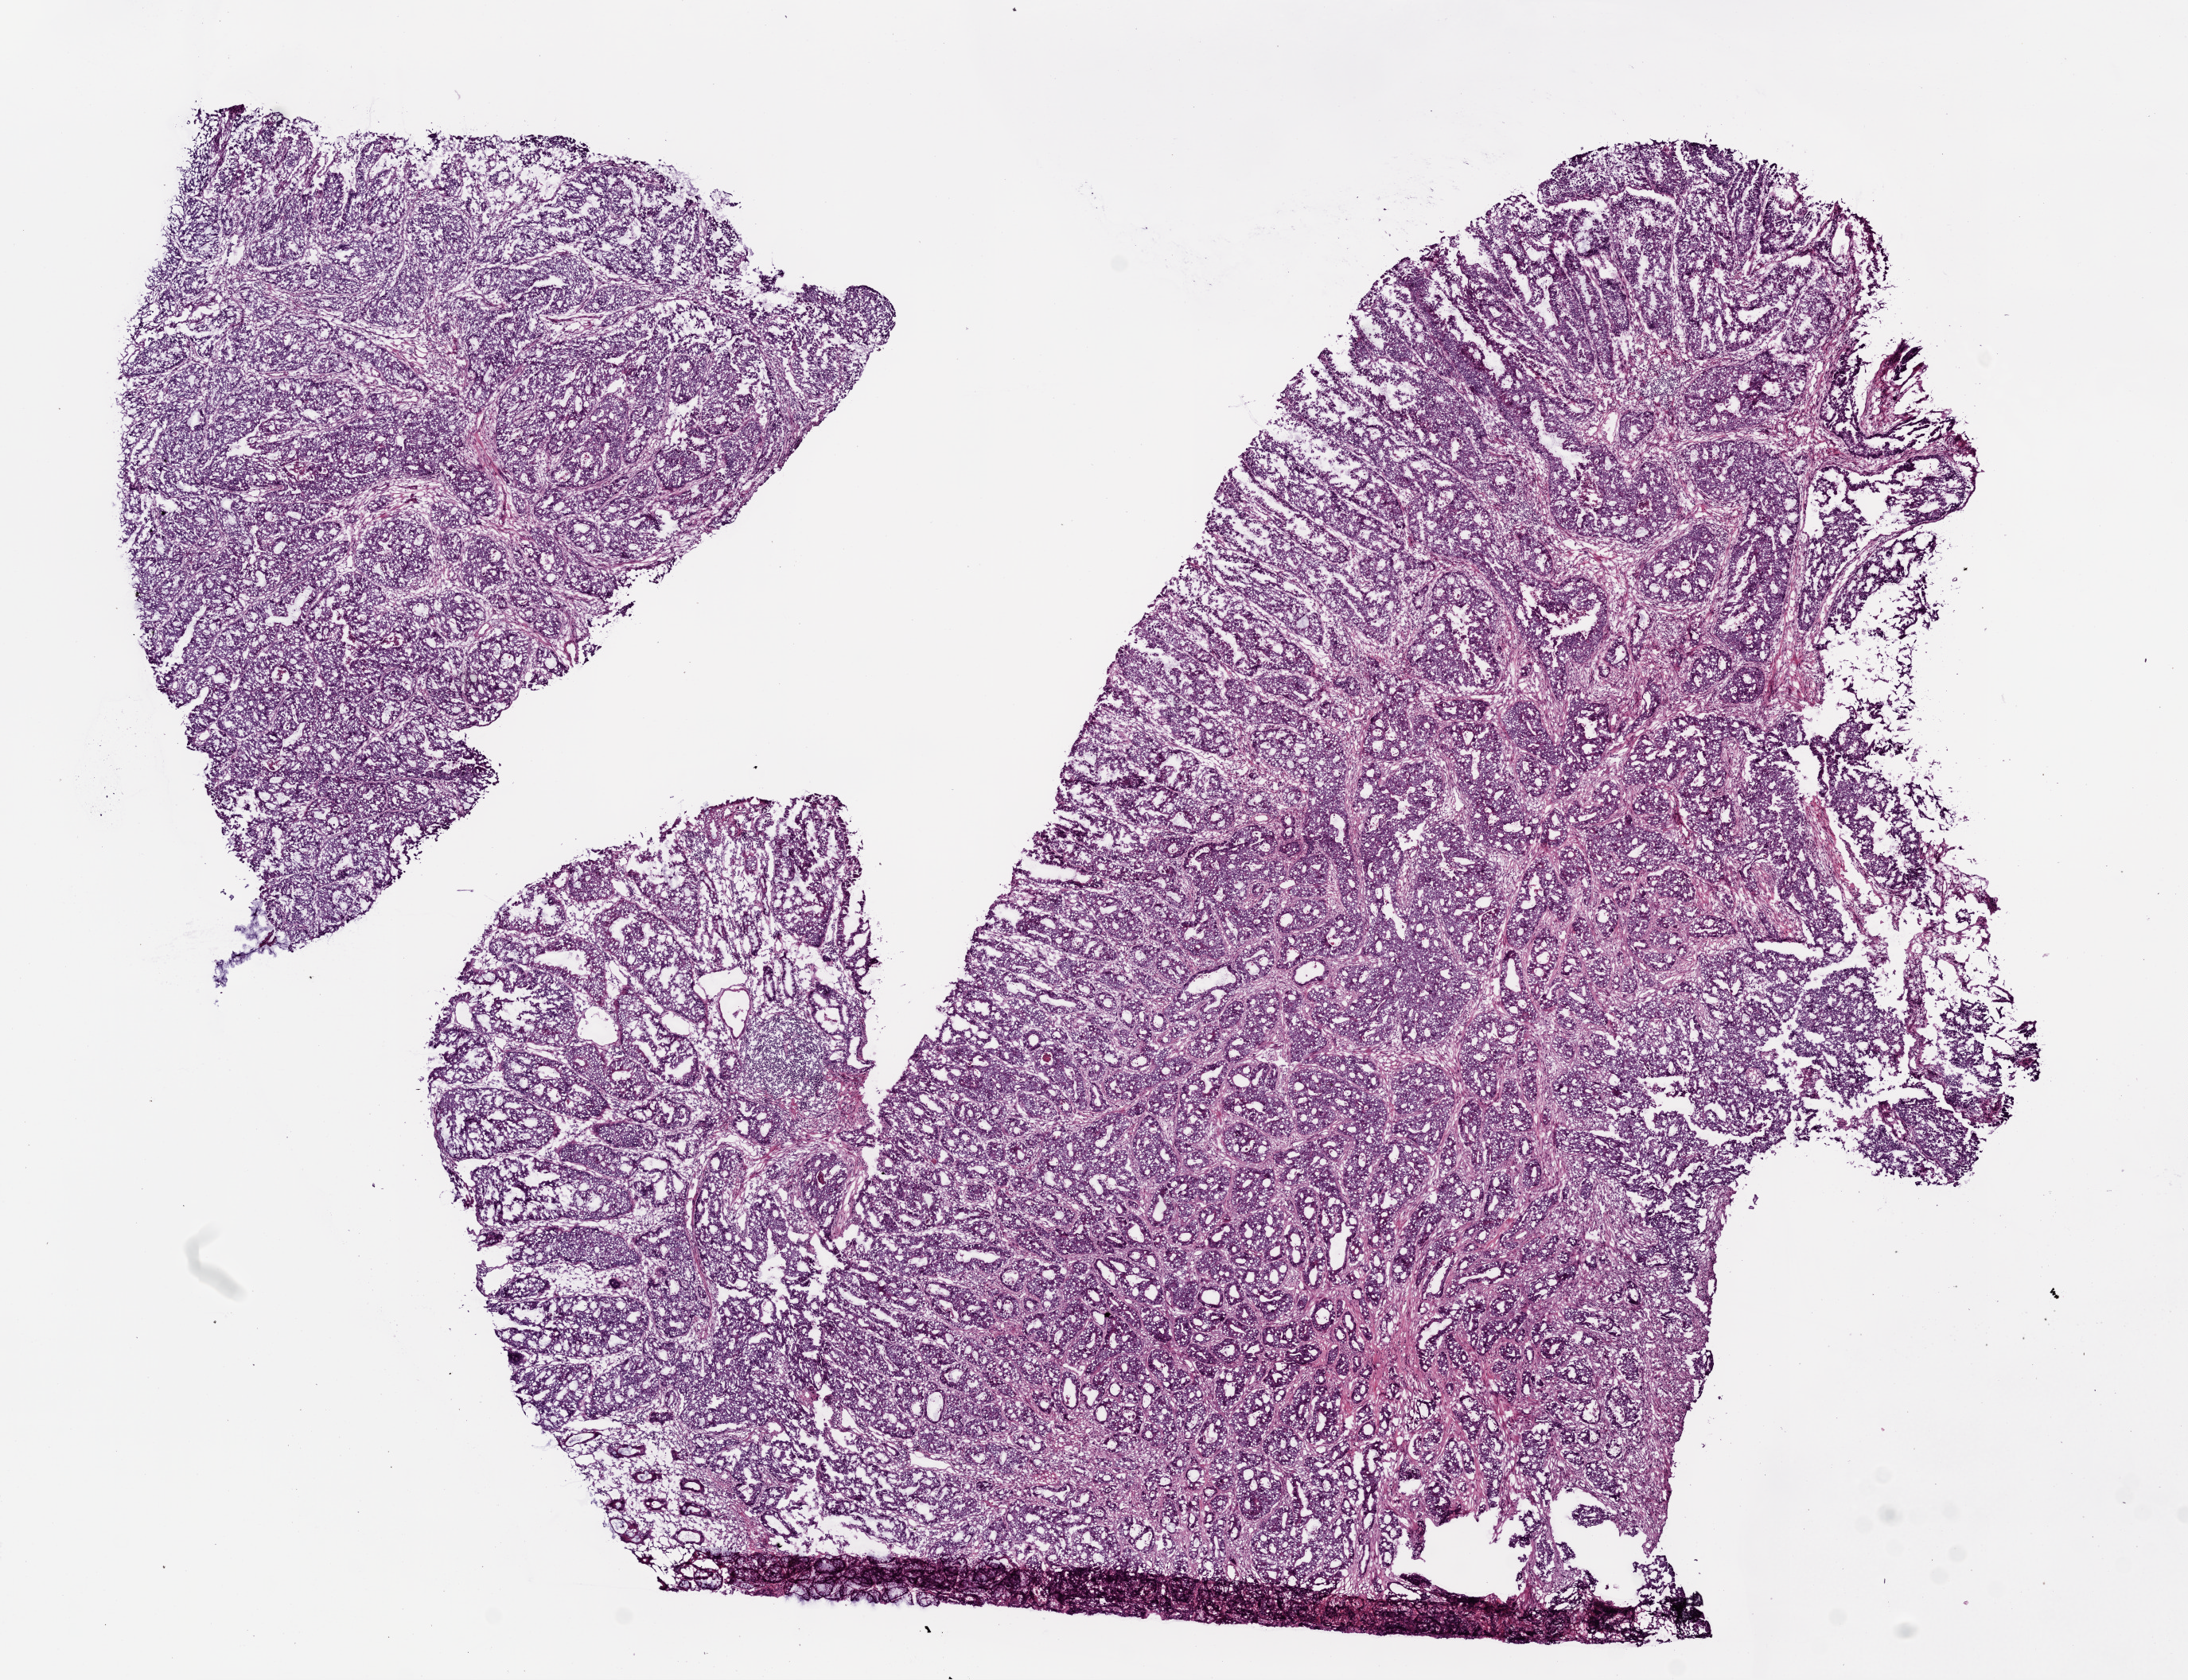
Digitized H&E tissue section (whole slide) — a low-resolution overview of the entire scanned area, about 11.0 x 8.5 mm (slide scanned at 20x). Frozen section from the top of the tissue portion. Primary tumour sample from the colon. Female patient; age at initial diagnosis 79 years. Composition of this section per pathologist review: tumour cells 70%, tumour nuclei 80%, normal cells 15%, stromal cells 10%, necrosis 5%.
• AJCC pathologic stage: IIA
• pathologic diagnosis: Adenocarcinoma, NOS